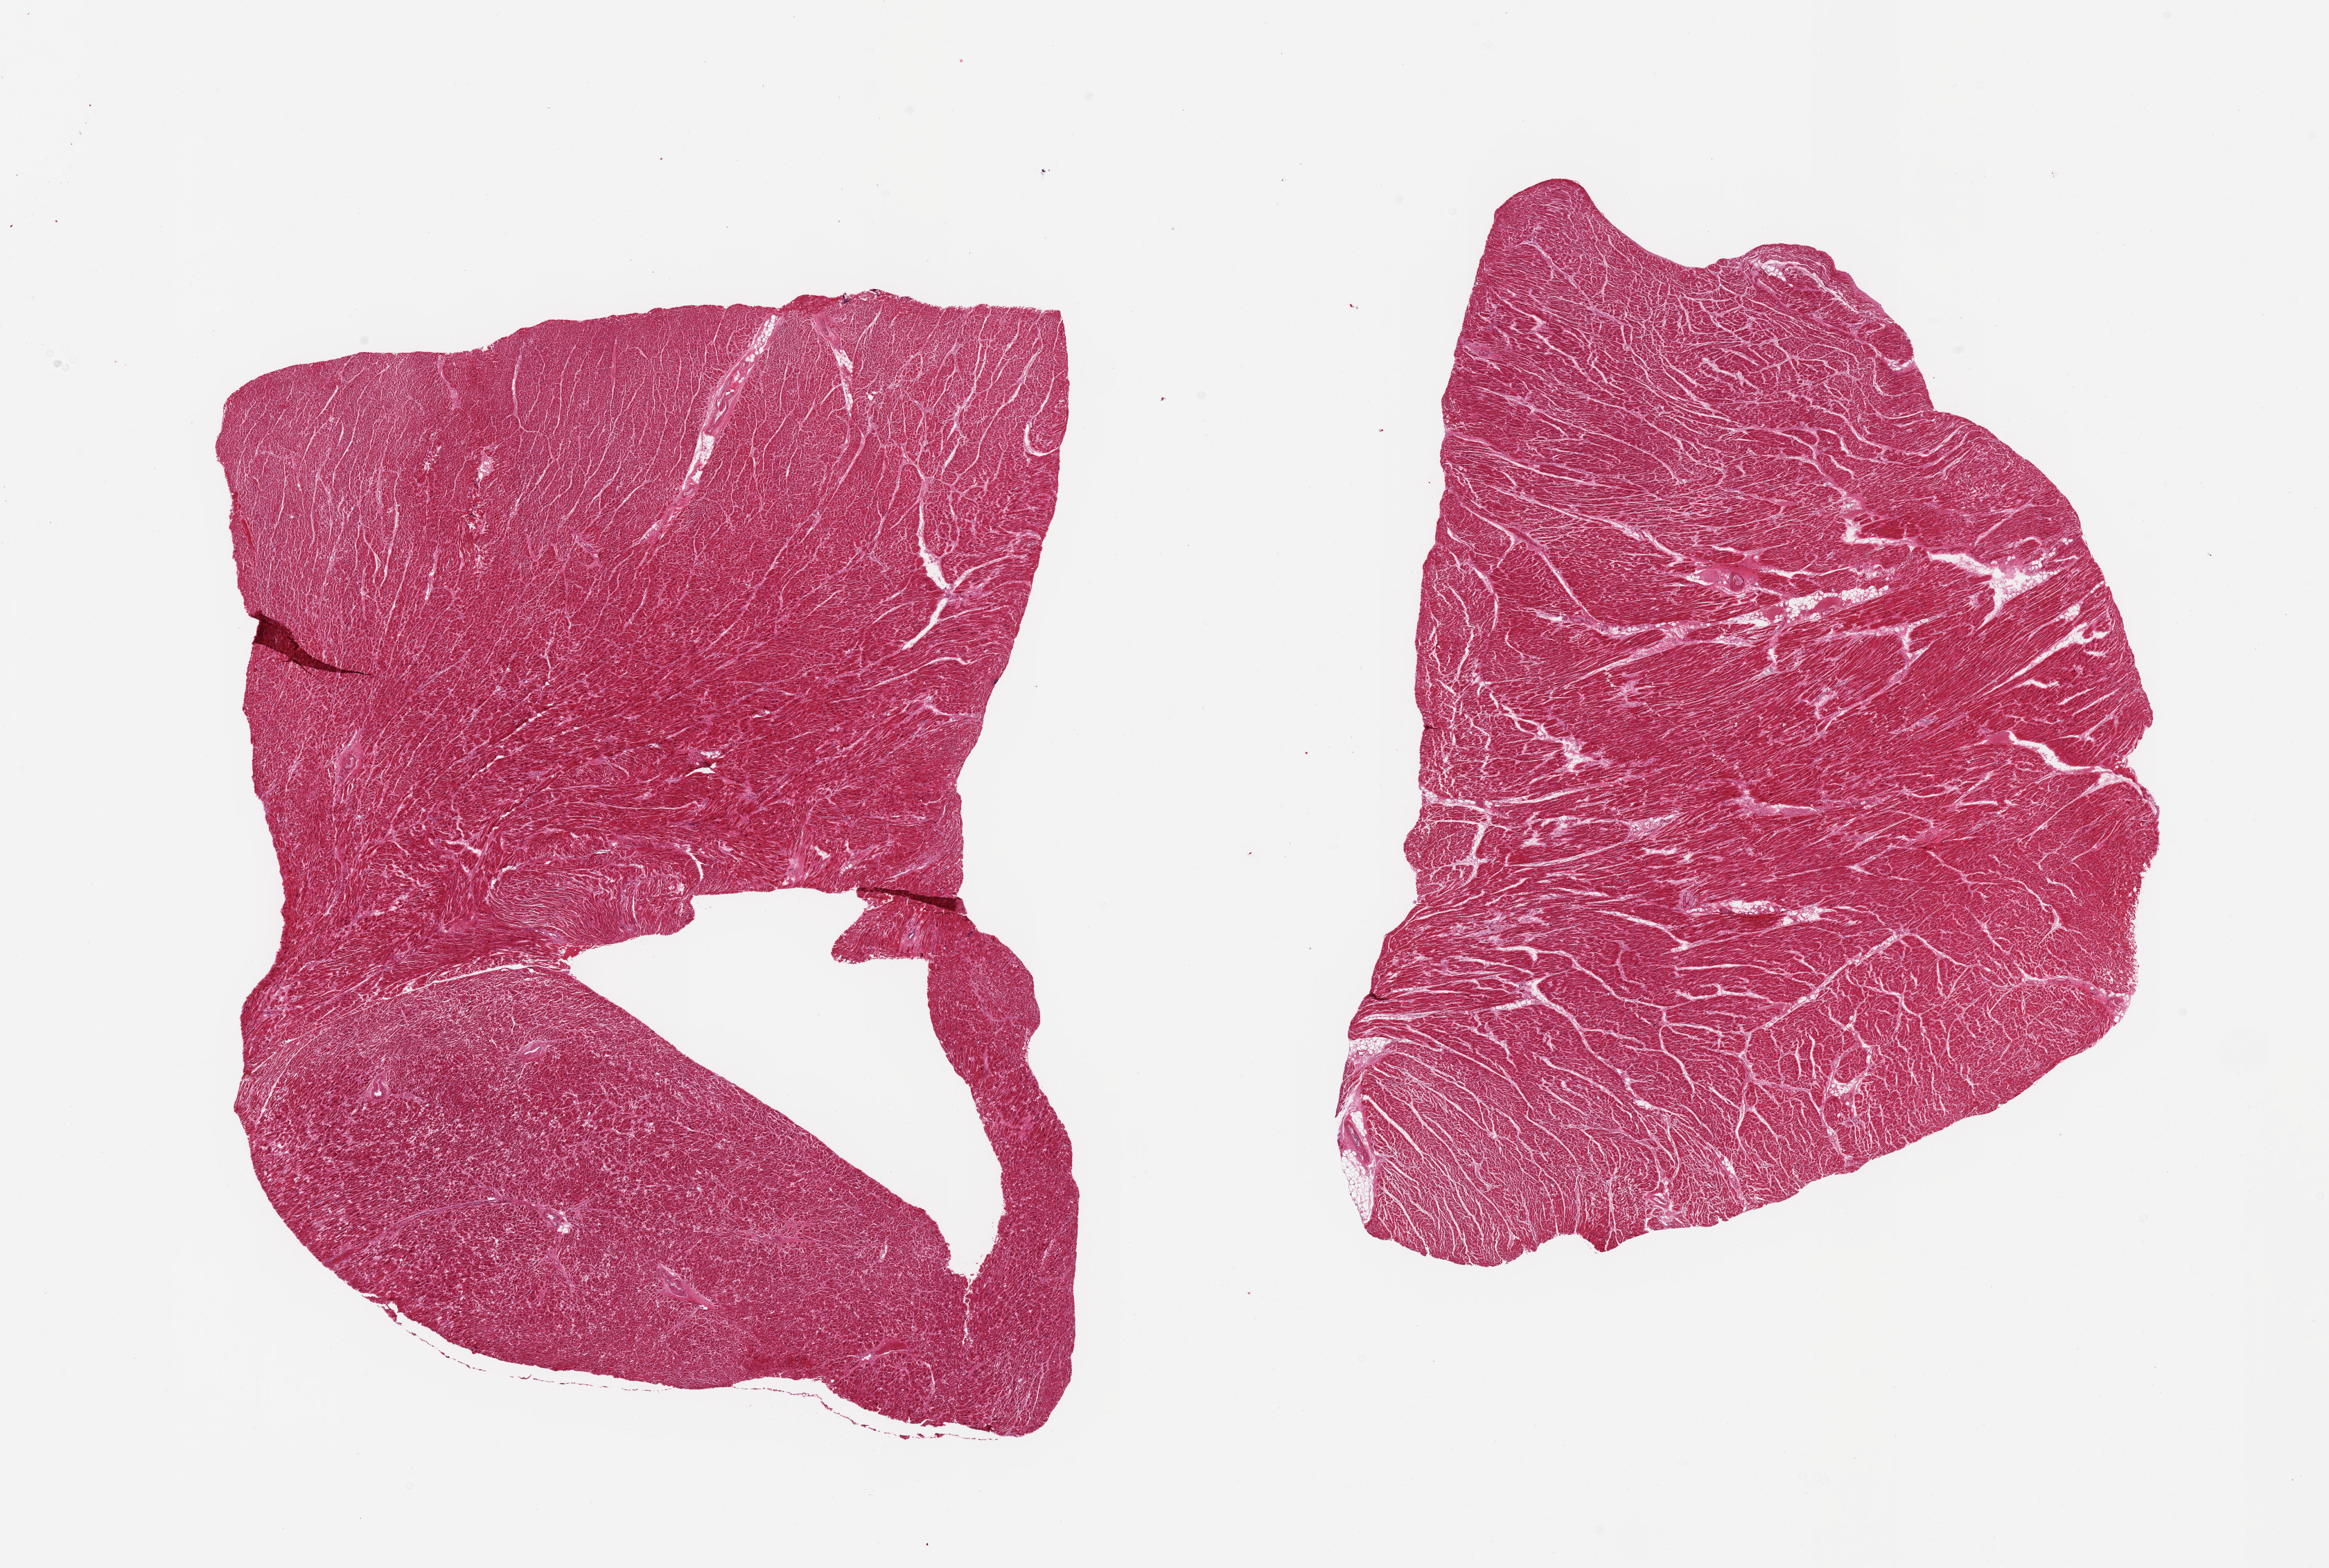
Whole-slide image, hematoxylin and eosin (H&E) stain, low-resolution overview of the scanned area, about 26.6 x 17.9 mm; PAXgene-fixed paraffin-embedded (PFPE) section; section of heart (target tissue); donor tissue sample.
* reviewer comment on this tissue sample: 2 pieces, minimal interstitial fibrosis